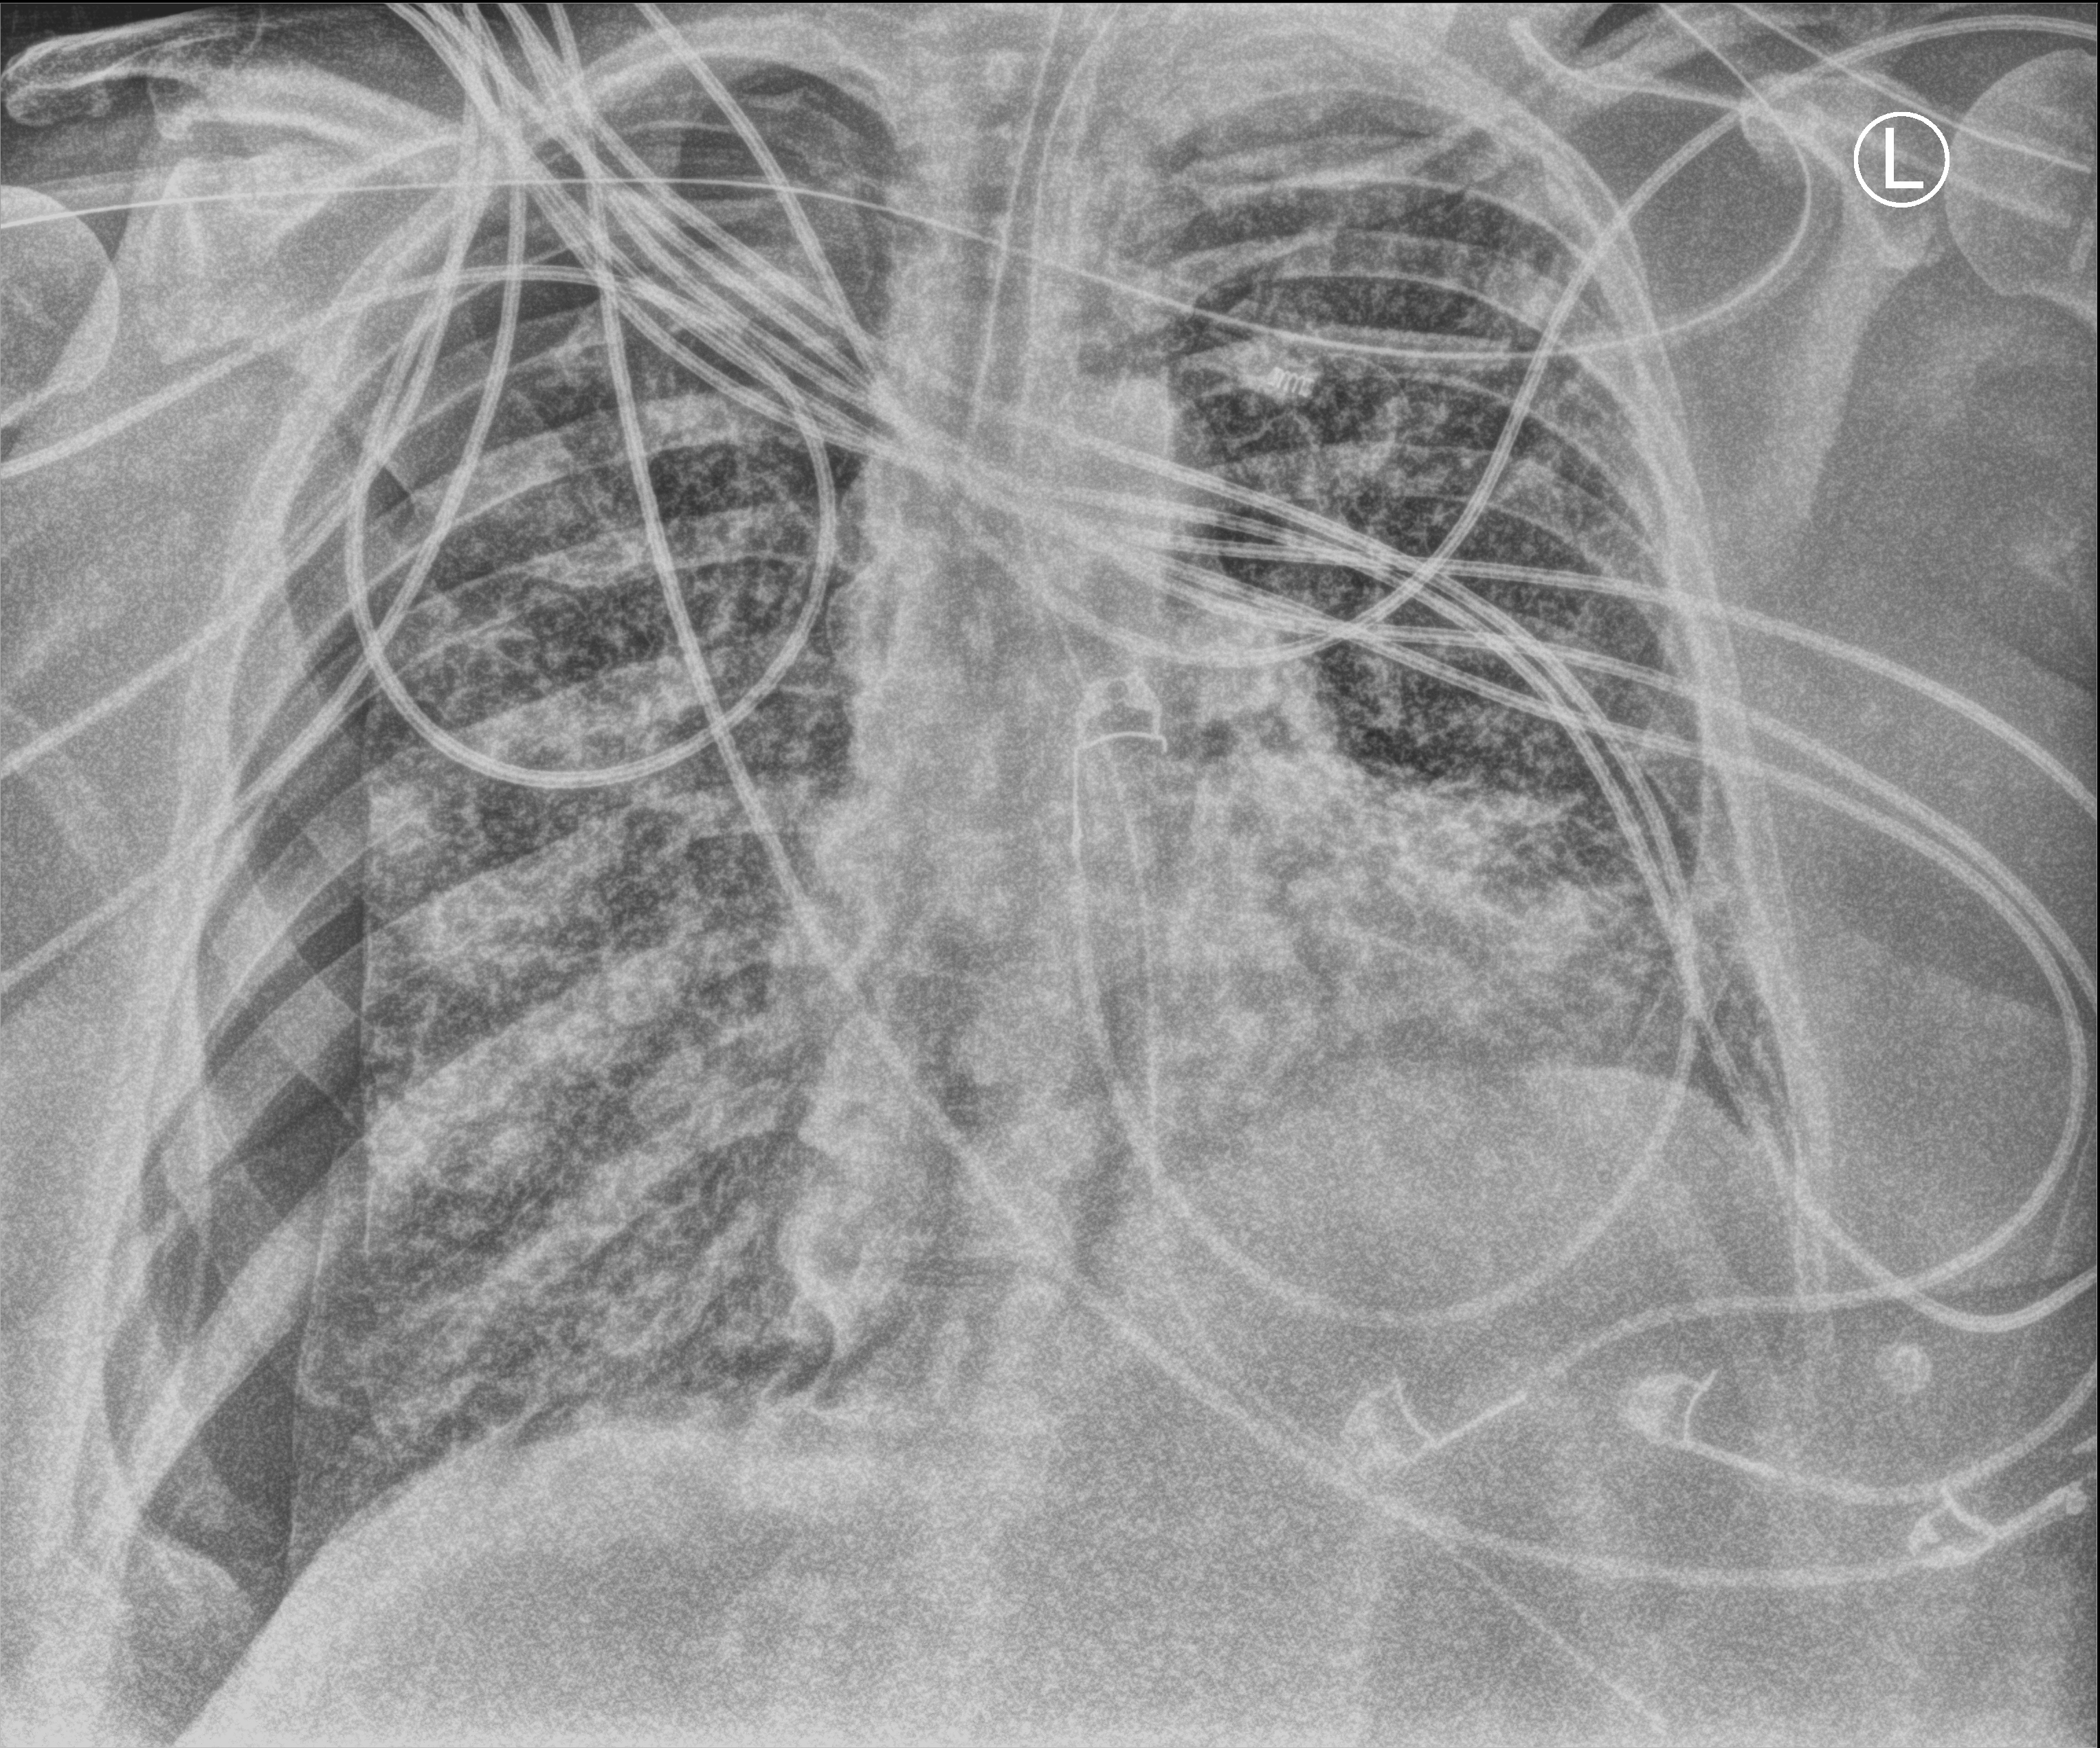
Bedside chest radiograph (computed radiography), anteroposterior (AP) projection. Patient hospitalised with COVID-19, aged 18–59 years.
From the hospital-stay record, not from the radiograph (when in the stay this image was taken is not recorded): length of hospital stay: 28 days.